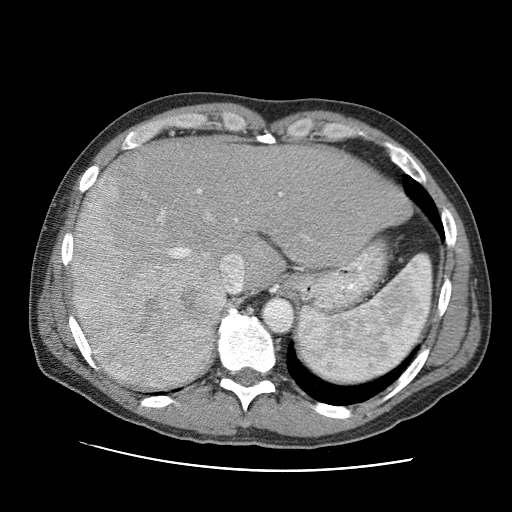
Contrast-enhanced abdominal CT (liver protocol), one axial slice. Slice 72 of 95 in the series (ordered by position). 120 kVp. One of 2 acquisitions stored at this slice position. Soft-tissue window (W 400 / L 40 HU). 2.5 mm slice thickness. 512 × 512 image matrix, field of view 360 × 360 mm. From the clinical record (not read from this slice): diagnosis: hepatocellular carcinoma (patient treated with transarterial chemoembolisation; whether this scan precedes or follows treatment is not stated here); TNM stage (as recorded): Stage-IVA; Child-Pugh class: A; tumour differentiation: moderately differentiated.
Outlined on this slice (semi-automatically segmented with operator editing):
- liver parenchyma outside the tumour (the mass and vessels are separate outlines, so this box may not span the whole liver): bounding box (x1, y1, x2, y2) in pixels: (71, 138, 412, 388)
- mass: (68, 174, 227, 391)
- liver vessels: (158, 189, 283, 222)